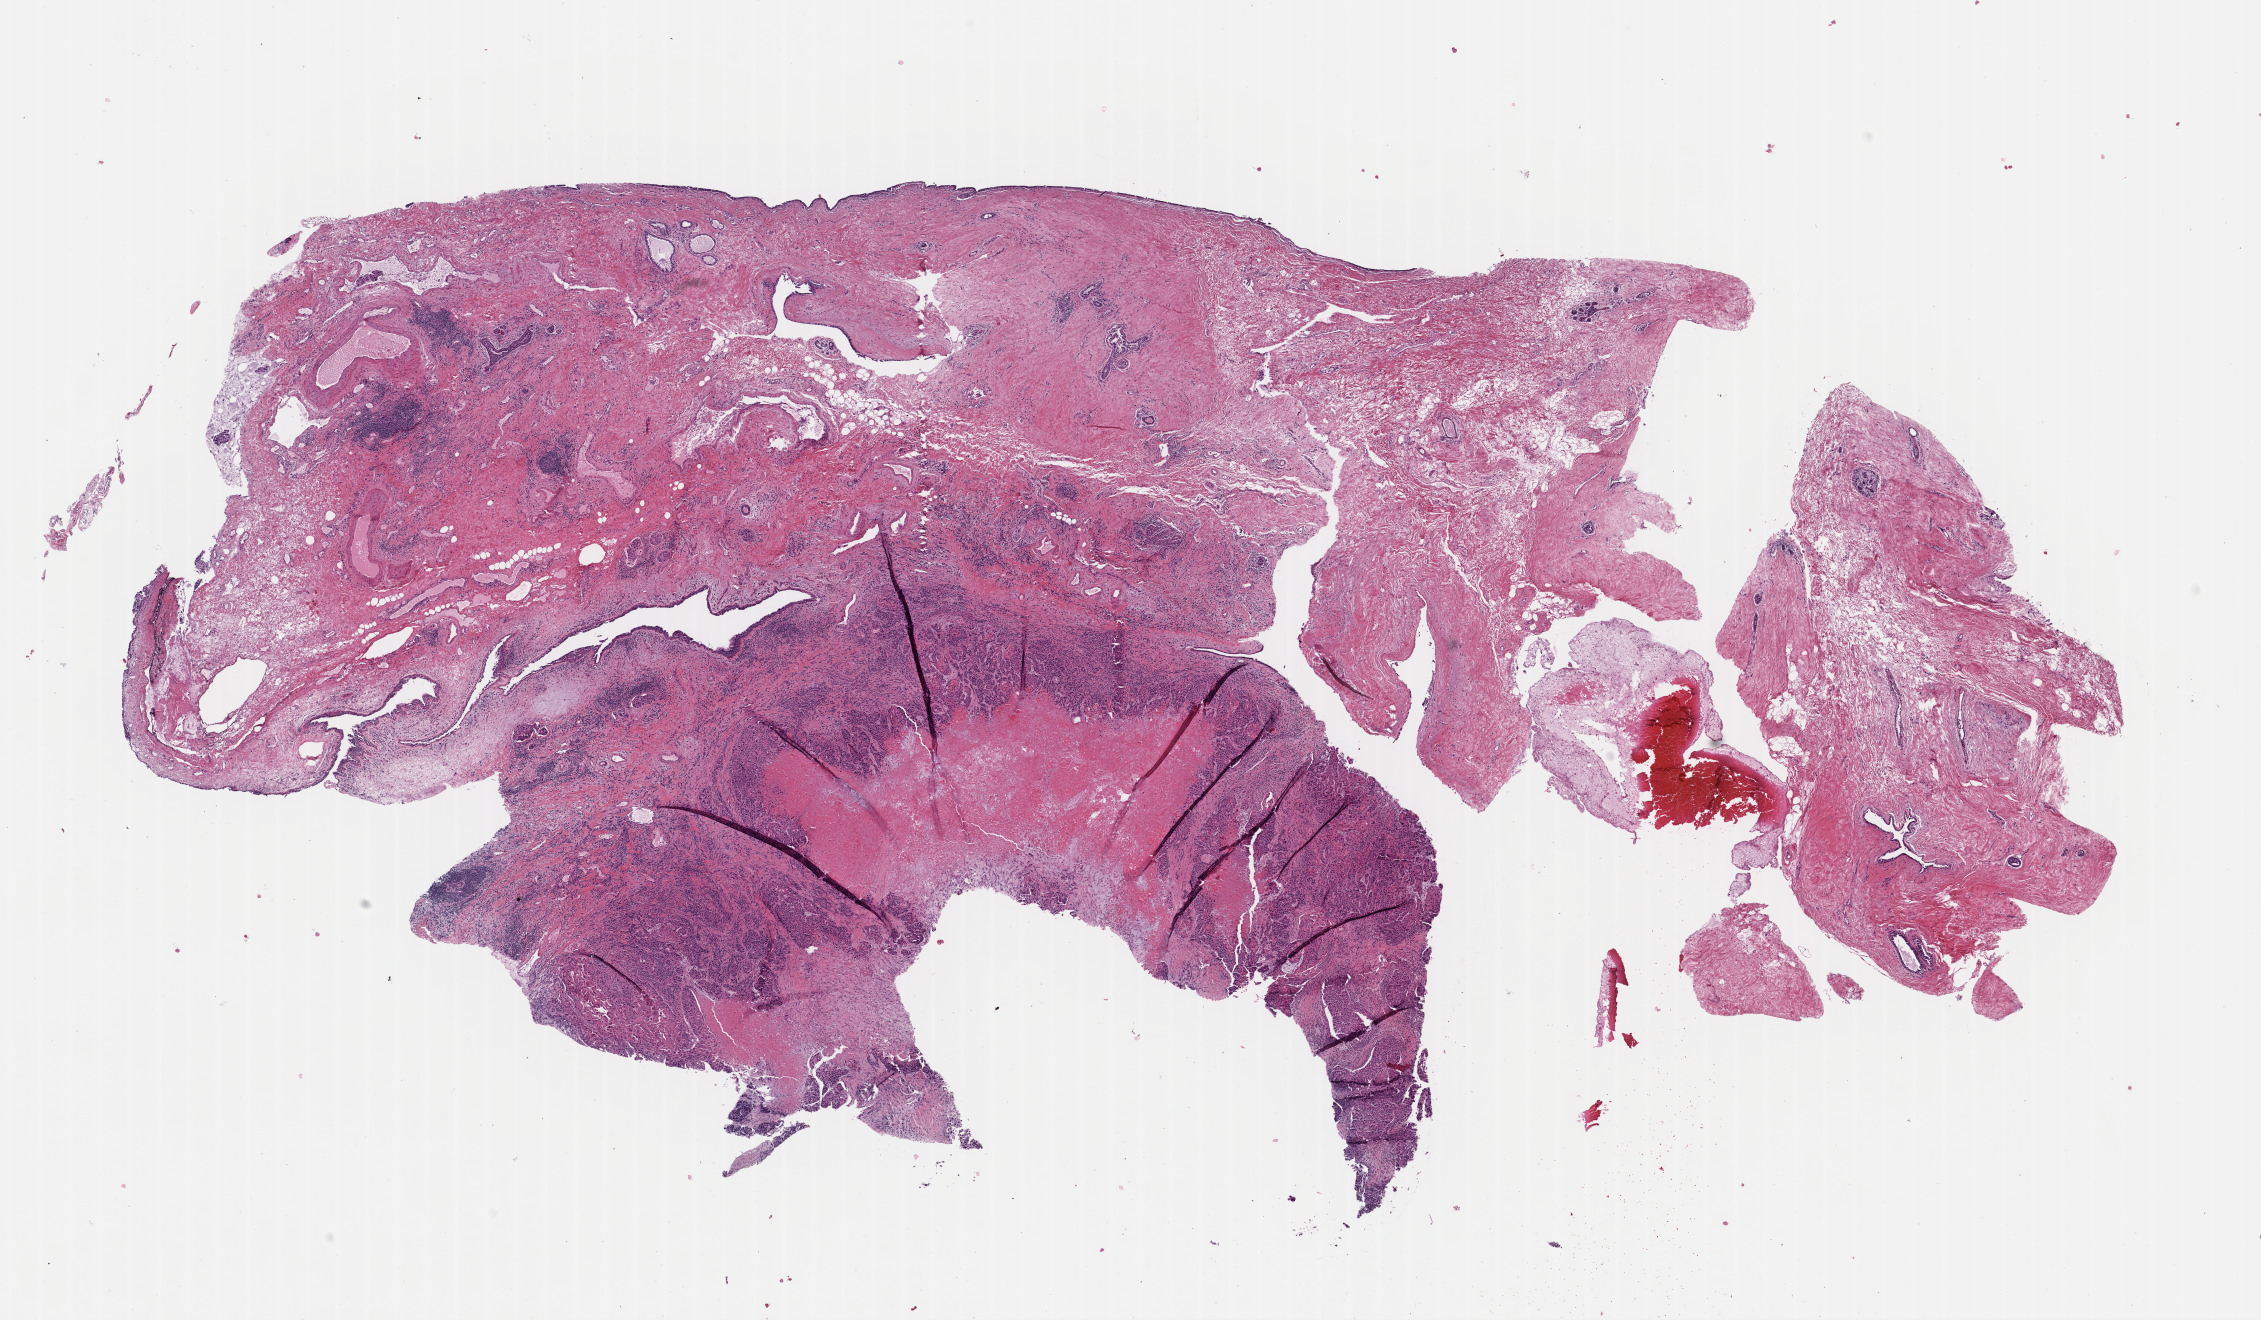
Digitized H&E tissue section (whole slide) — whole scanned area (about 17.9 x 10.4 mm, from a 40x scan) shown as a low-resolution overview, formalin-fixed paraffin-embedded (FFPE) diagnostic section, breast, primary tumour sample. Female, age 73 years at initial diagnosis.
• laterality: left
• AJCC pathologic stage: IIB
• histologic diagnosis: Infiltrating duct carcinoma, NOS
• TNM: T2 N1 M0
• lymph nodes positive (case pathology): 0 of 4 examined